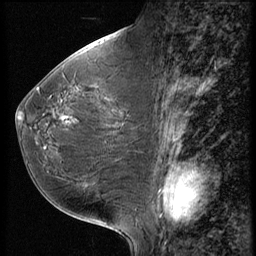
Breast MRI (dynamic contrast-enhanced), one sagittal slice; position 26 of 56 along the scan axis; 3 images stored at this slice position (order not interpretable as contrast timing); 1.5 T; TE 4.2 ms, TR 9 ms; 2.5 mm slice thickness; 256 × 256 image matrix, field of view 180 × 180 mm. Patient: female, 49 years. From the clinical record (not read from this slice): setting: breast cancer imaged before/during neoadjuvant chemotherapy; receptor status: HER2-positive.
Annotated regions visible in this slice (semi-automatically segmented with operator editing):
- analysis volume of interest (the breast-tissue region the enhancement analysis was run in; not a lesion): bounding box <17,74,148,198> (left, top, right, bottom; pixels)
- tumour enhancement mask (voxels above the 140 % enhancement threshold inside the analysis volume of interest): <18,113,76,124>